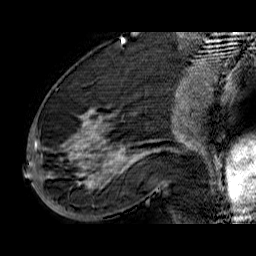
Breast MRI (dynamic contrast-enhanced), one sagittal slice. Slice 26 of 60 in the series (ordered by position). Dynamic contrast-enhanced series, time point 2 of 6 at this slice position (early post-contrast). 1.5 T. TE 6.5 ms, TR 32.9 ms. 4 mm slice thickness. 256 × 256 image matrix, field of view 200 × 200 mm. Female patient. From the clinical record (not read from this slice): setting: breast cancer imaged before/during neoadjuvant chemotherapy; receptor status: HR-positive, HER2-negative.
Annotated regions visible in this slice (semi-automatically segmented with operator editing):
- analysis volume of interest (the breast-tissue region the enhancement analysis was run in; not a lesion): bounding box (x1, y1, x2, y2) in pixels: (33, 74, 176, 210)
- tumour enhancement mask (voxels above the 100 % enhancement threshold inside the analysis volume of interest): (34, 109, 146, 188)